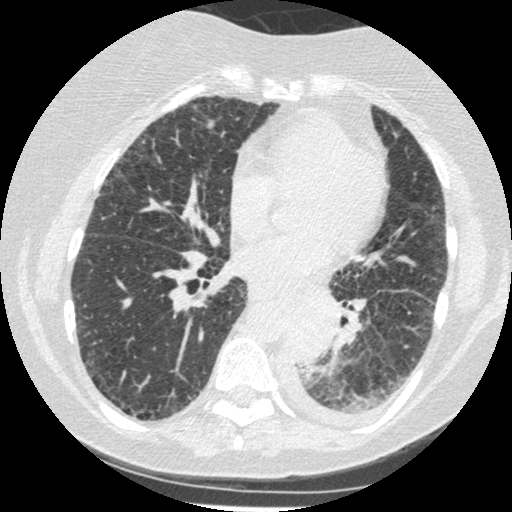
Axial slice from a low-dose chest CT screening exam. Third screening round (two years after baseline). Lung window (W 1500 / L -600 HU). Standard (soft-tissue) reconstruction kernel (STANDARD). 120 kVp. Slice 242 of 341 in the series. Female, age 60 years at enrolment. Former smoker at enrolment.
- Expert reader's lesion annotation, box from (x=276, y=303) to (x=343, y=376) px.
- Reader record for this screening exam (exam-level; its link to the box is not recorded): non-calcified nodule or mass ≥4 mm, left lower lobe, 54 × 38 mm, smooth margins, soft tissue attenuation, pre-existing on the prior screen: yes; interval growth: yes.
- Official screen result: positive, other.
- Participant outcome: lung cancer diagnosed 15 days after this screen — small cell carcinoma, NOS, left lower lobe, undifferentiated (G4), stage IV (AJCC 6th edition), 69 mm at pathology.